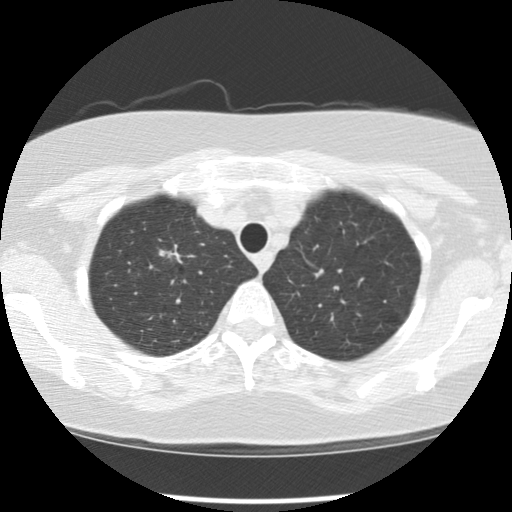
Low-dose screening chest CT, one axial slice. Position 95 of 113 along the scan axis. 120 kVp. Lung window (W 1500 / L -600 HU). 512 × 512 image matrix.
Structures marked on this image (outlined manually by an expert reader):
- lesion 1 (tumor, upper lobe of right lung): bounding box <159,248,182,263> (left, top, right, bottom; pixels)